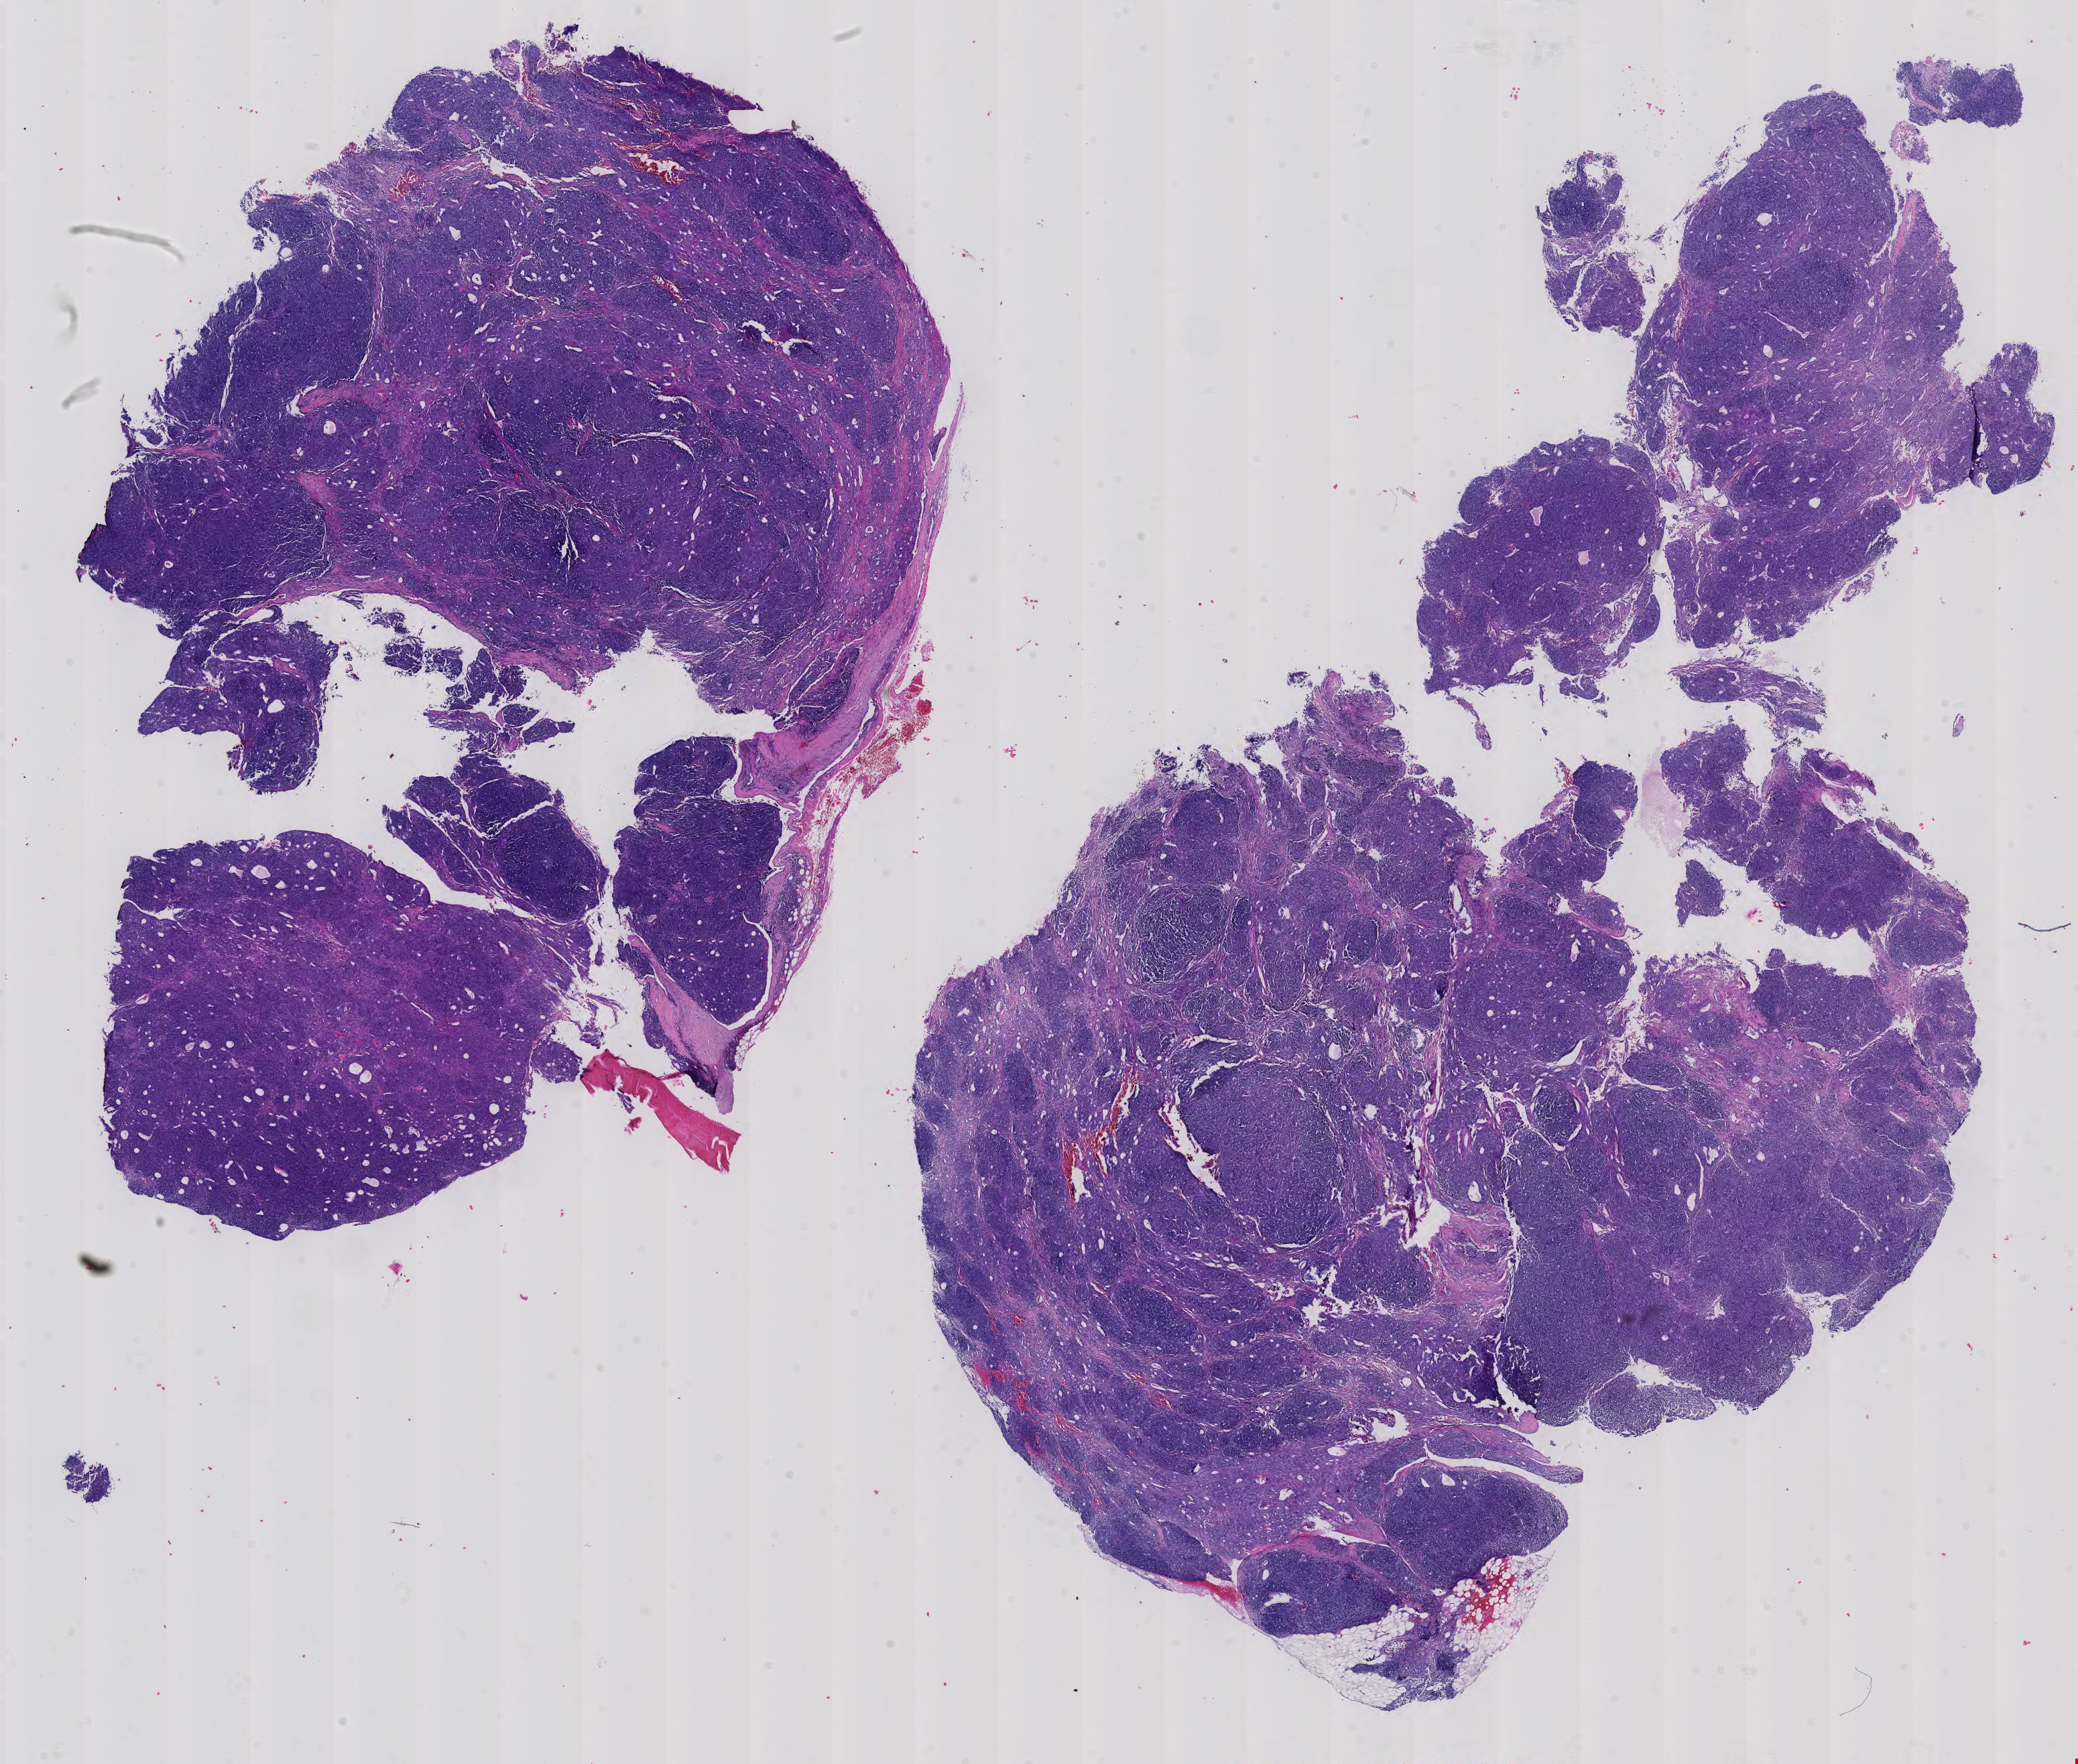
Whole-slide histology image, Hematoxylin and eosin (H&E) stained, a low-resolution overview of the entire scanned area, about 22.6 x 19.2 mm; formalin-fixed paraffin-embedded (FFPE) diagnostic section; sample: primary tumour, thymus. Male patient; age at initial diagnosis 49 years.
- histologic diagnosis: Thymoma, type AB, malignant